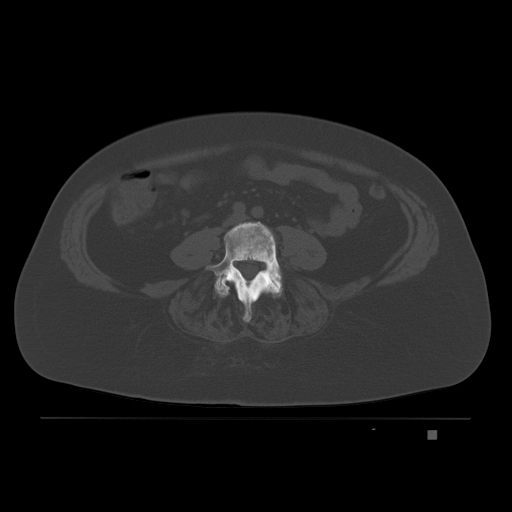
CT including the spine, one axial slice. Slice 40 of 221 in the series (ordered by position). Bone window (W 1800 / L 400 HU). 3 mm slice thickness. 512 × 512 image matrix, field of view 474 × 474 mm. Patient: female, 63 years. From the clinical record (not read from this slice): primary cancer: breast.
Outlined on this slice (semi-automatic segmentation, software-assisted and operator-edited):
- L4 vertebra: bounding box (x1, y1, x2, y2) in pixels: (206, 221, 282, 323)
- L5 vertebra: (215, 275, 282, 297)